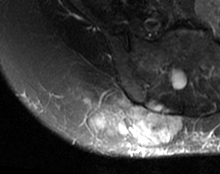
MRI of an extremity soft-tissue mass, one axial slice. Slice 43 of 63 in the series (ordered by position). T2-weighted fat-saturated. MR volume resampled by the dataset authors to the PET/CT grid (not the native acquisition matrix). 220 × 174 image matrix, field of view 215 × 170 mm. Female patient. From the clinical record (not read from this slice): histological type: spindle cell suggestive of myxofibrosarcoma; grade: intermediate; site of the primary tumour: right buttock.
Annotated regions visible in this slice (expert contour drawn on MRI and transferred to this co-registered scan by the dataset authors):
- gross tumour volume (mass): bounding box (x1, y1, x2, y2) in pixels: (84, 97, 183, 147)